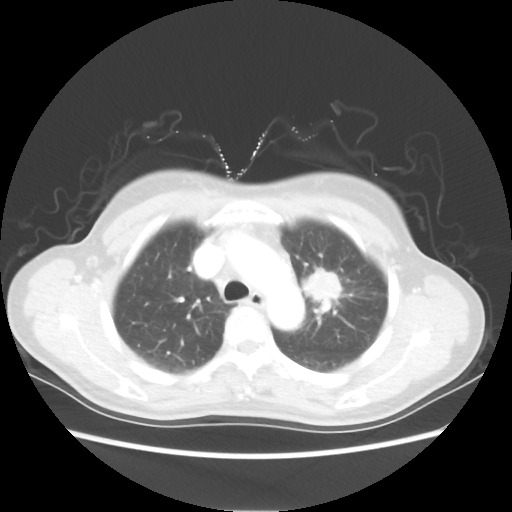
Chest CT, one axial slice; slice 40 of 54 in the series (ordered by position); reconstruction kernel STANDARD; lung window (W 1500 / L -600 HU); 5 mm slice thickness; 512 × 512 image matrix, field of view 360 × 360 mm. Patient: female, 53 years. From the clinical record (not read from this slice): clinical TNM (as recorded): T1c N0 M0.
Structures marked on this image (bounding box drawn by a radiologist):
- lung tumour (recorded histology: adenocarcinoma): bounding box (x1, y1, x2, y2) in pixels: (298, 260, 354, 309)
- lung tumour (recorded histology: adenocarcinoma): (307, 265, 342, 304)